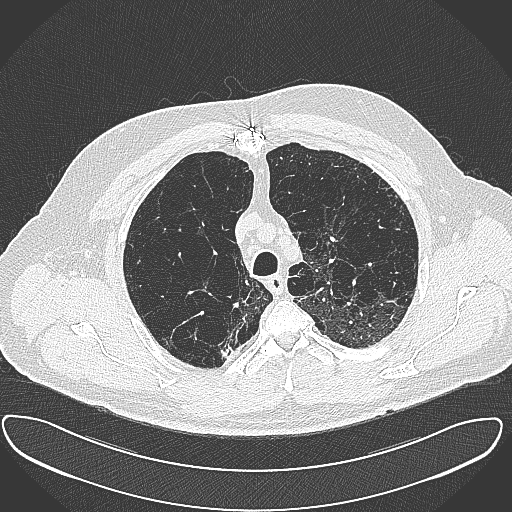
Chest CT (low-dose screening protocol), one axial image; baseline screening round; lung window (W 1500 / L -600 HU); 512 × 512 image matrix. Male, age 60 years at enrolment.
• Lesion marked by an expert reader, bounding box <202,327,240,362> (left, top, right, bottom; pixels).
• Reader record for this screening exam (exam-level; its link to the box is not recorded): non-calcified nodule or mass ≥4 mm, right upper lobe, 15 × 25 mm, spiculated (stellate) margins, soft tissue attenuation.
• Lung cancer was diagnosed 32 days after this screen: carcinoma, NOS, right upper lobe, moderately differentiated (G2), stage IB (AJCC 6th edition), 35 mm at pathology.